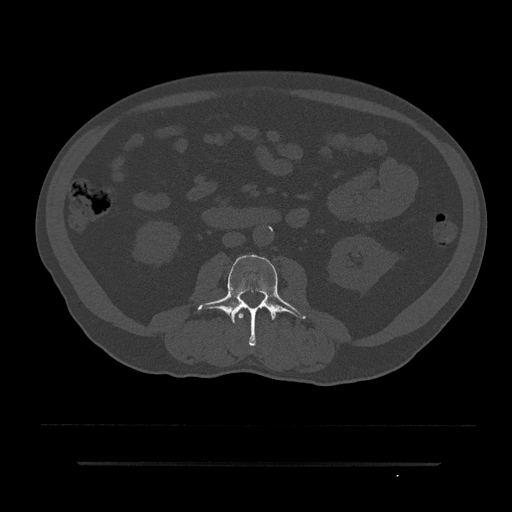
CT including the spine, one axial slice; slice 12 of 797 in the series (ordered by position); reconstruction kernel Br40s/3; 120 kVp; bone window (W 1800 / L 400 HU); 0.5 mm slice thickness; 512 × 512 image matrix, field of view 464 × 464 mm. Male patient, age 59 years. From the clinical record (not read from this slice): primary cancer: bile ducts; vertebrae with lytic lesions (as recorded): T10.
Outlined on this slice (semi-automatically segmented with operator editing):
- L2 vertebra: bounding box (x1, y1, x2, y2) in pixels: (238, 308, 244, 319)
- L3 vertebra: (197, 254, 306, 346)